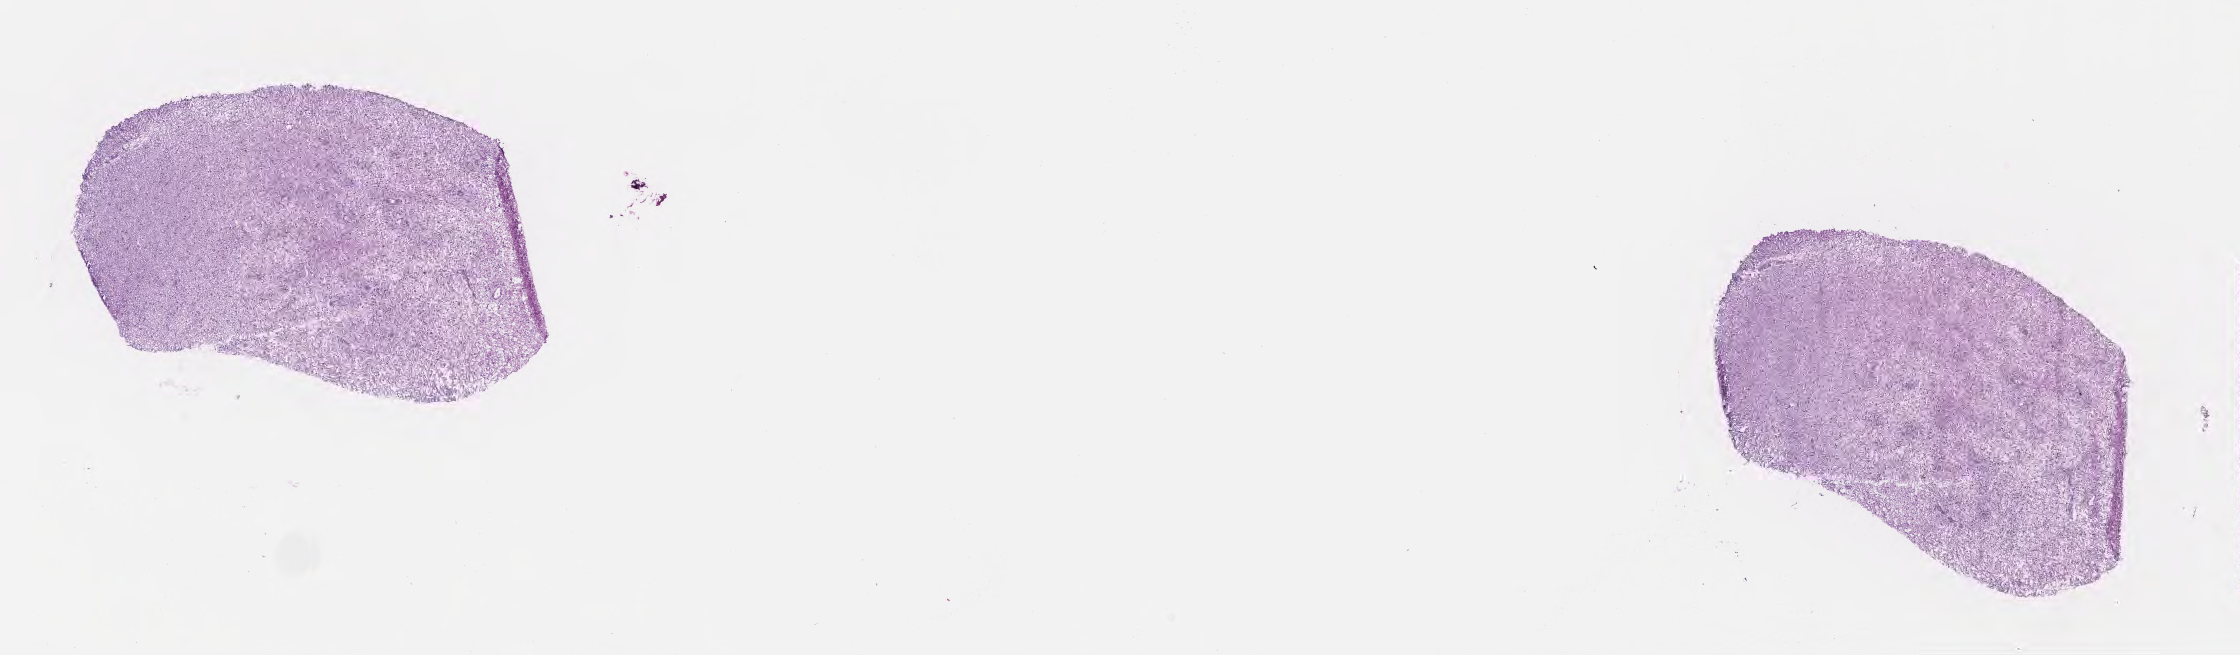
Digitized hematoxylin and eosin (H&E)-stained section — a low-resolution overview of the entire scanned area, about 18.1 x 5.3 mm. Frozen section (tissue freezing medium). Primary tumor. Site: brain. Male, age 54 years at initial diagnosis. Slide review estimates, as recorded: tumor cells 61%, tumor nuclei 80%, stromal cells 24%, necrosis 0%, normal cells 15%. Infiltration values recorded for this section: lymphocyte infiltration 0%, monocyte infiltration 0%, neutrophil infiltration 0%.
- diagnosis: Glioblastoma, NOS